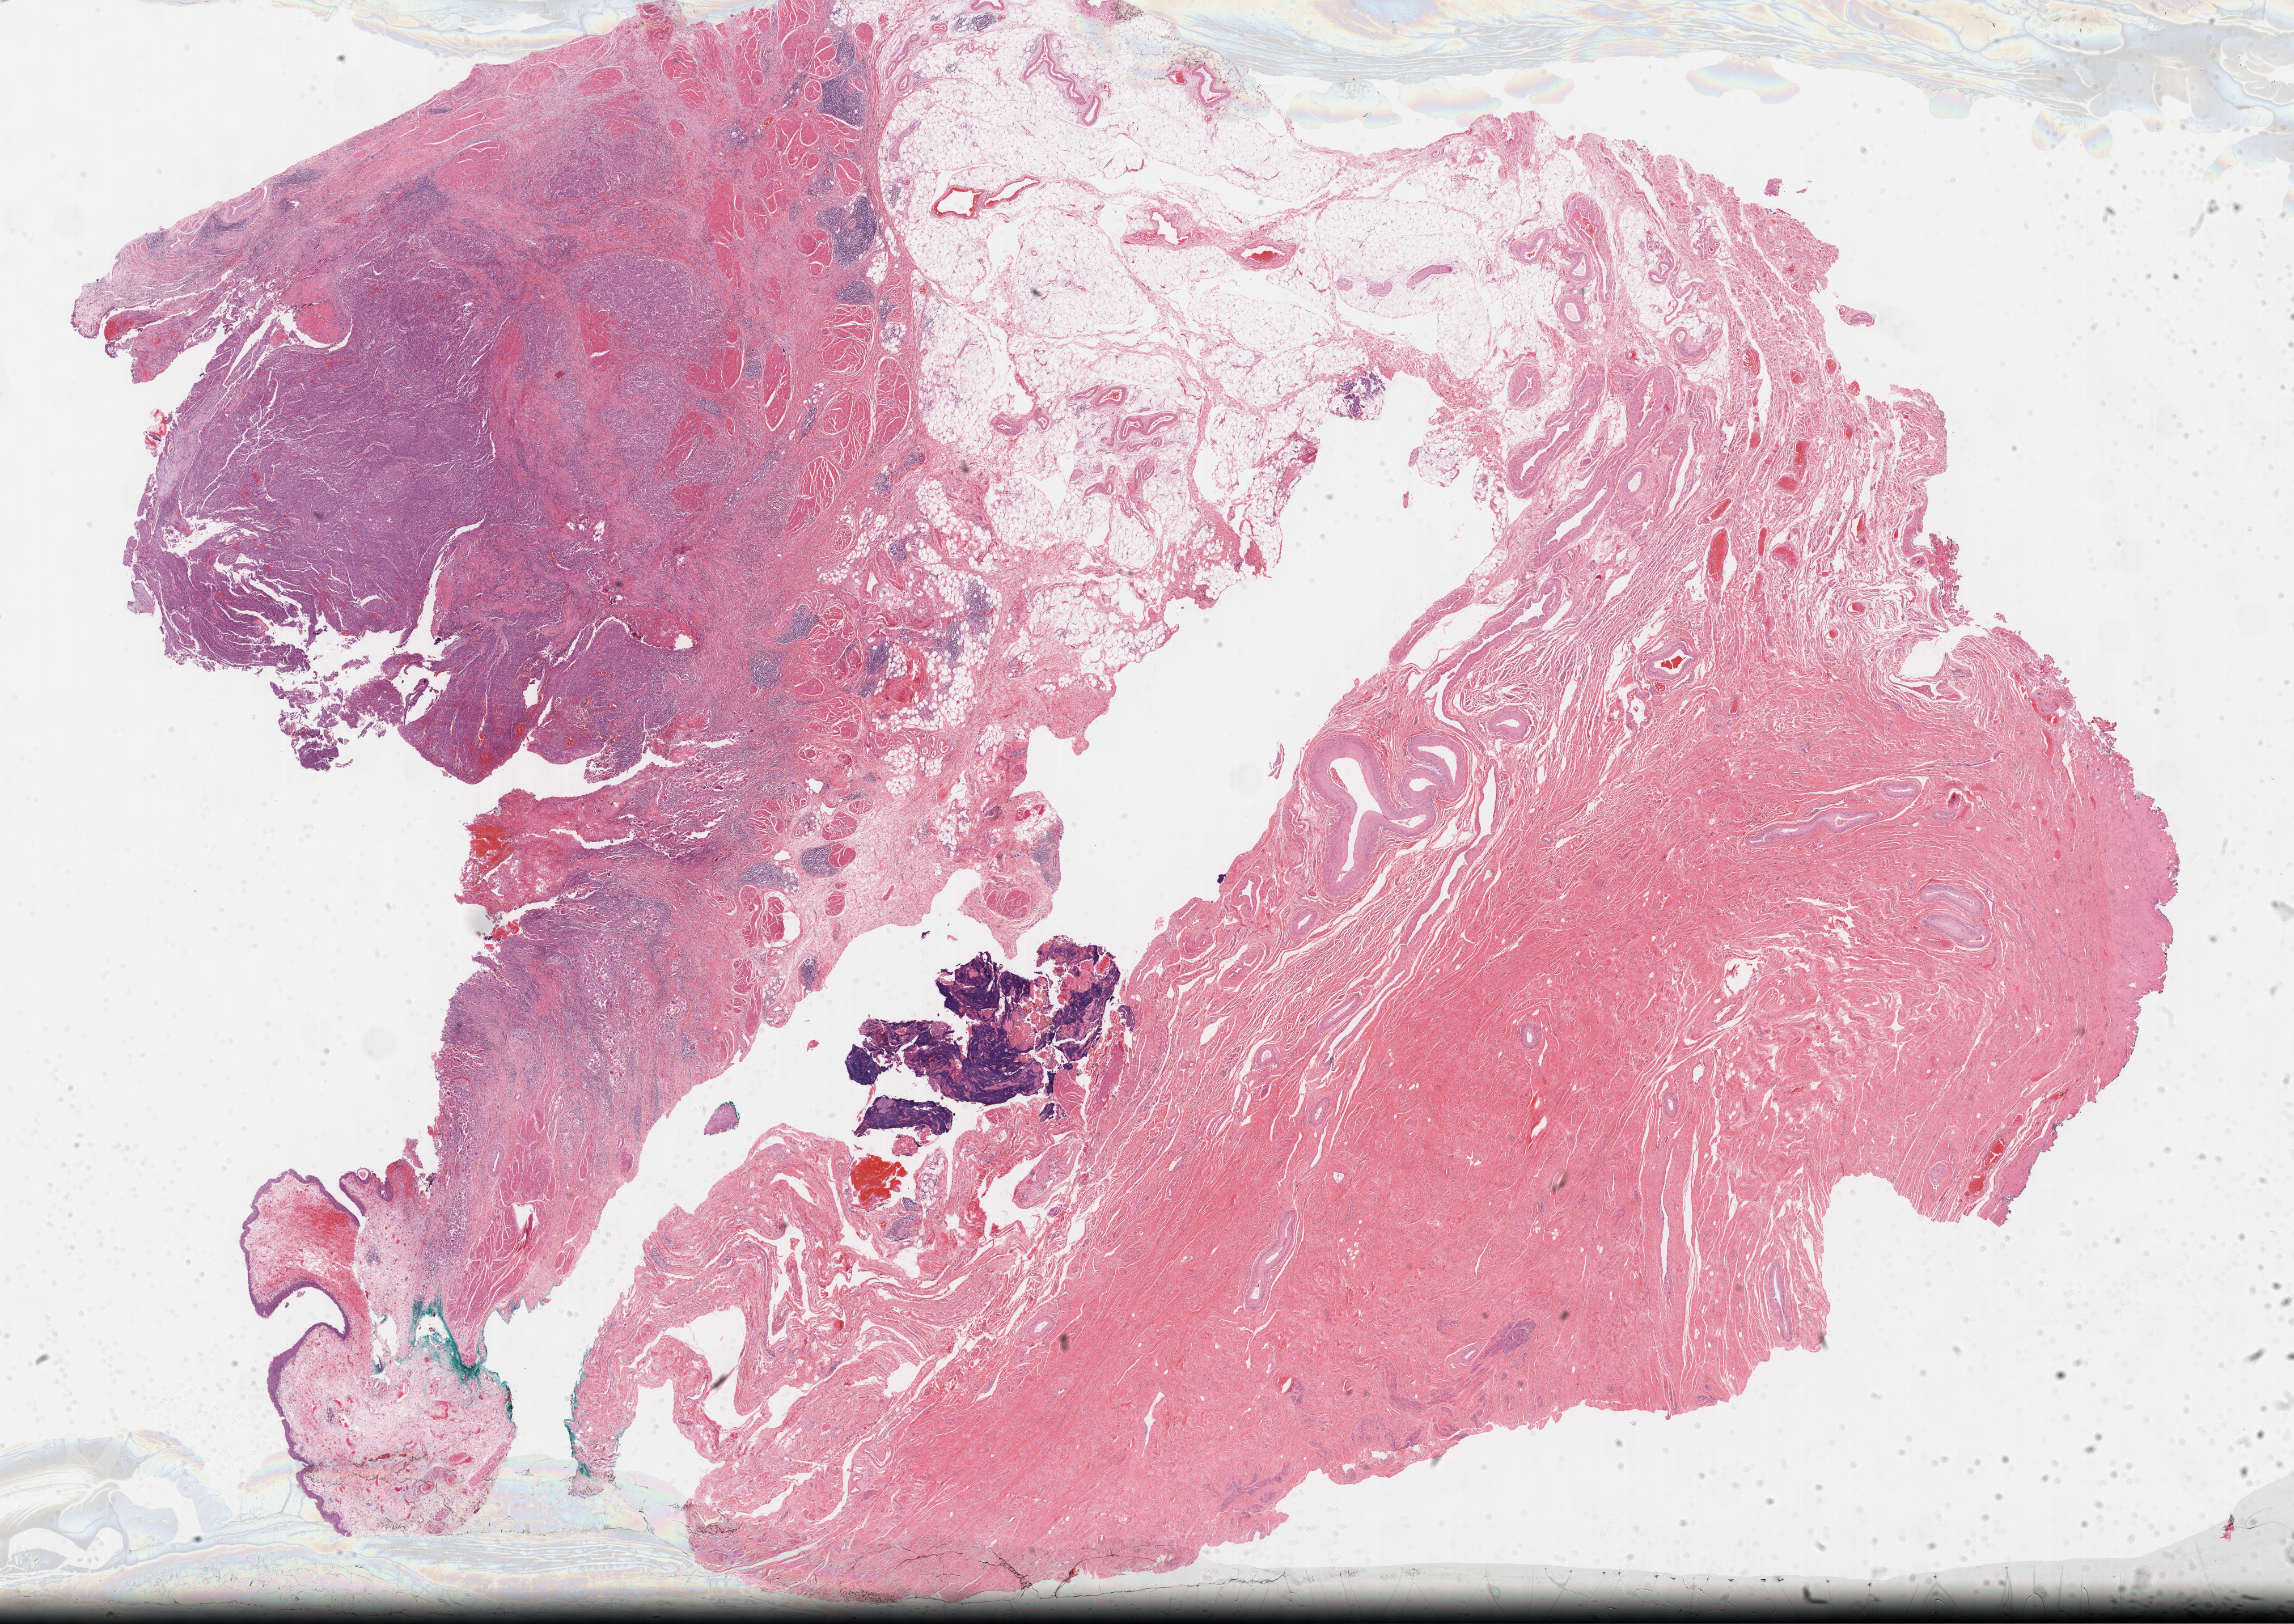
Digitized H&E-stained tissue section (whole slide) — shown as a low-resolution overview of the whole scanned area (about 32.7 x 23.2 mm, slide scanned at 40x), FFPE section, bladder, primary tumour sample. Female patient; age at initial diagnosis 78 years. Histologic grade: high grade.
Histologic diagnosis: Transitional cell carcinoma. AJCC pathologic stage: II (6th edition). TNM: T2 N0 MX.